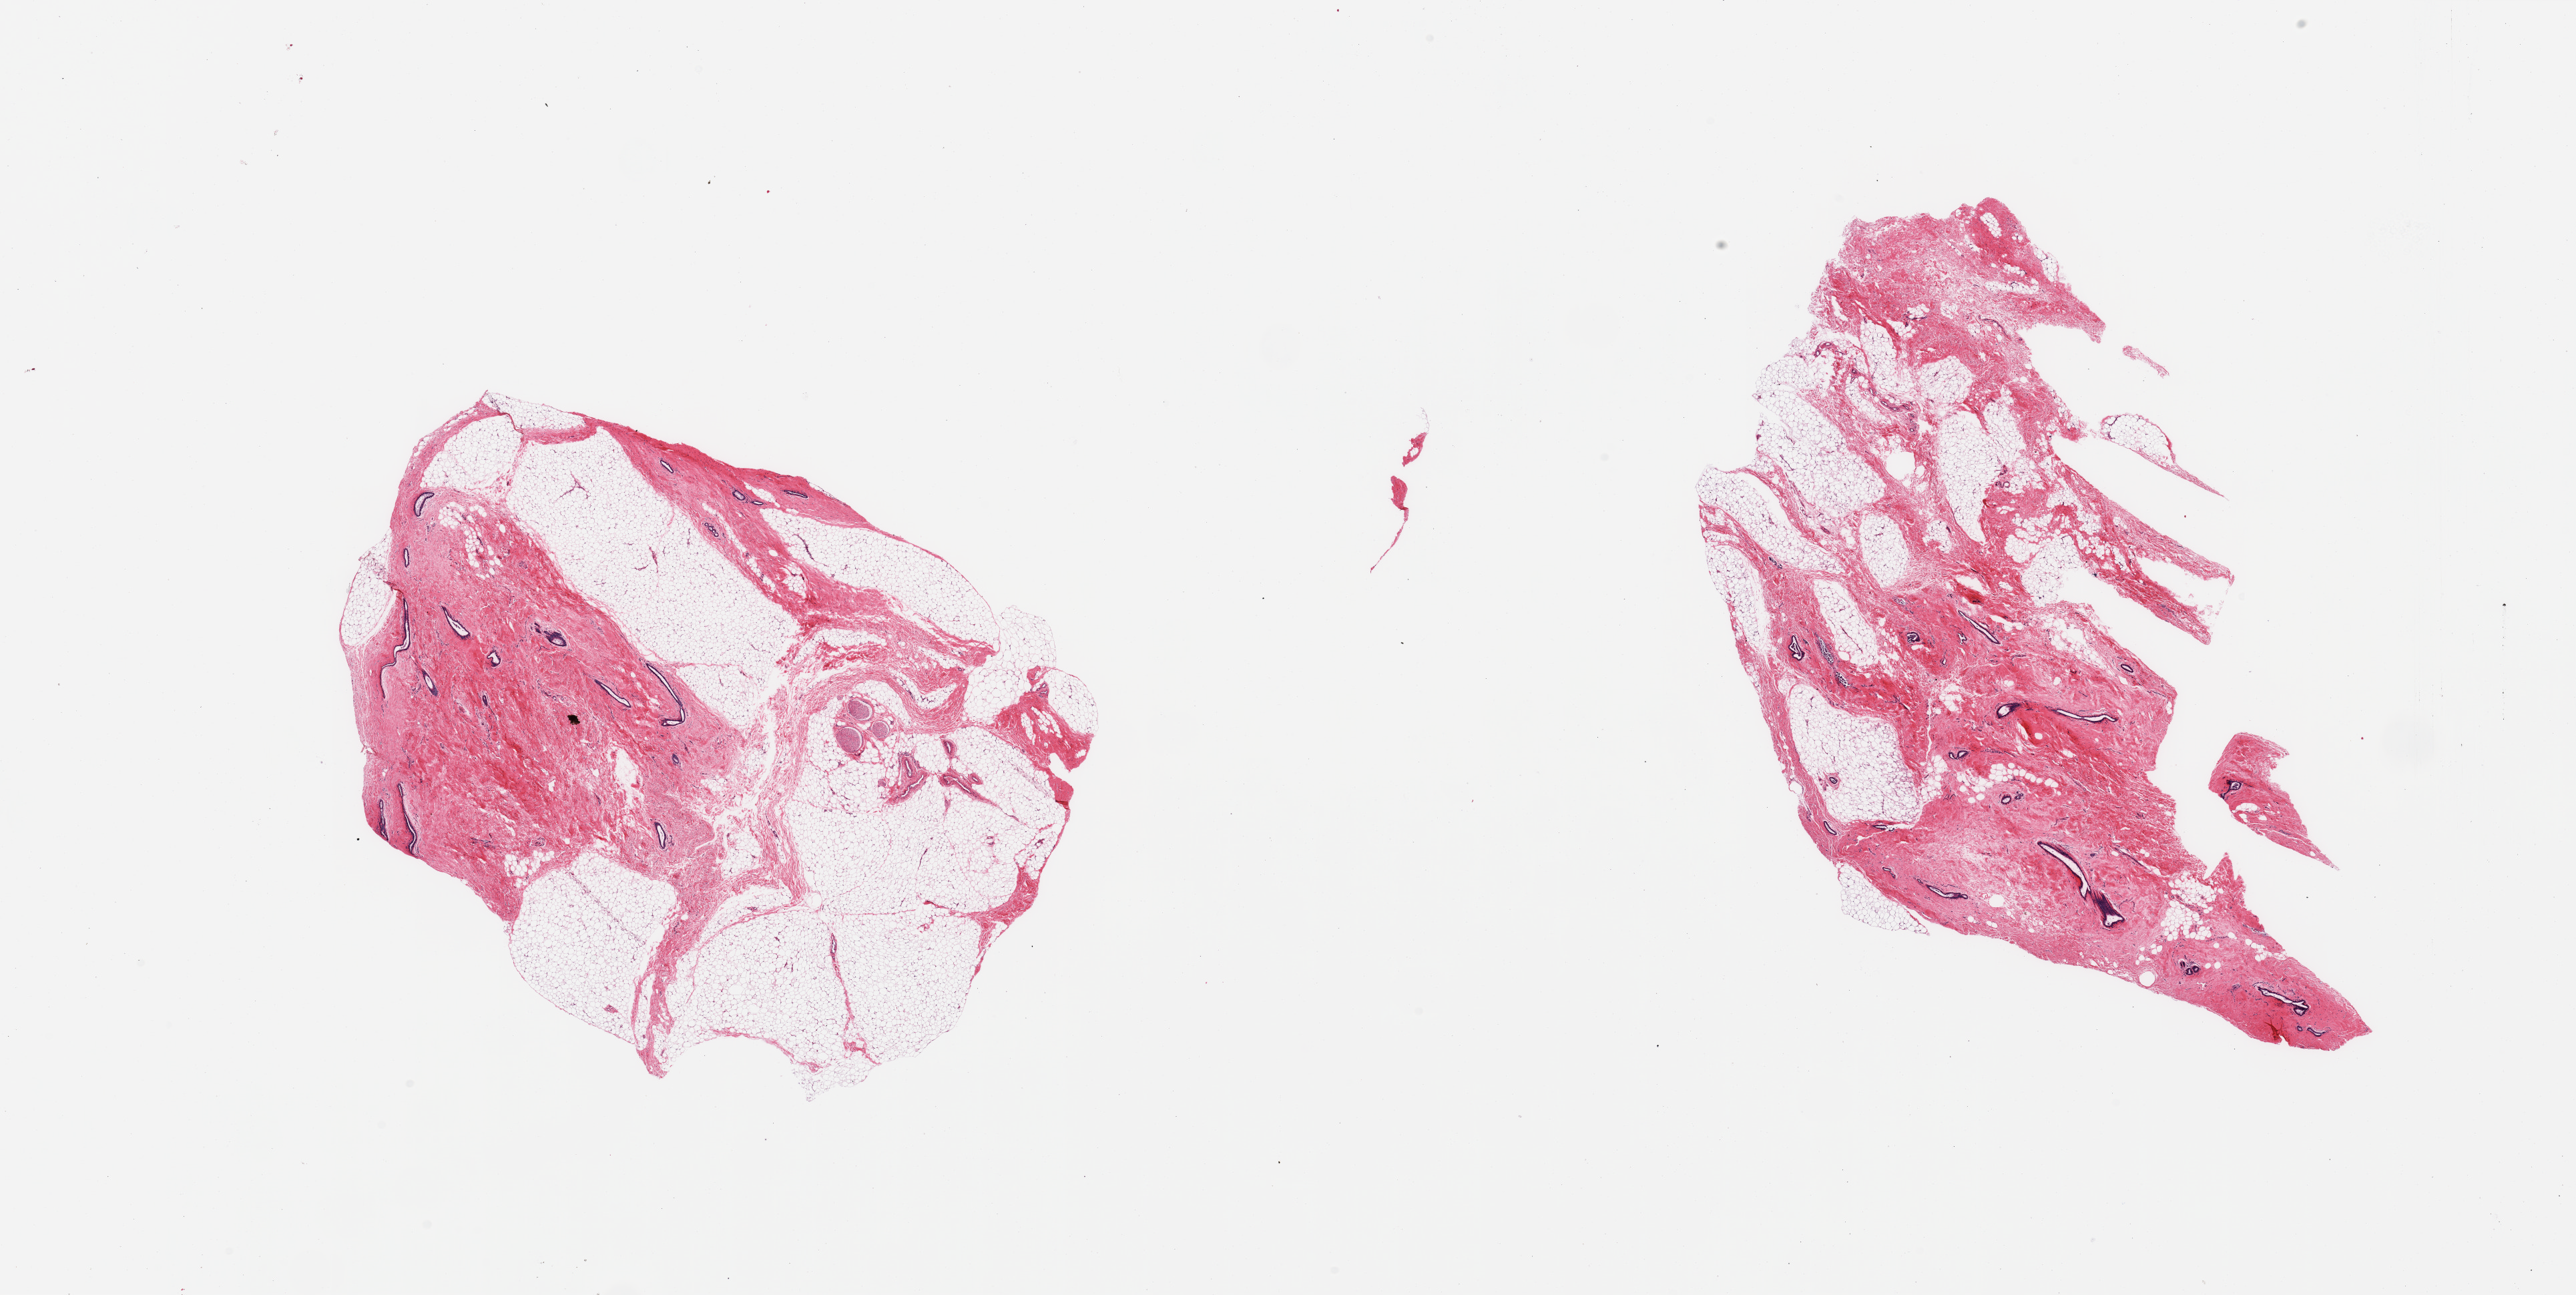
Whole-slide image, hematoxylin and eosin (H&E) stain, a low-resolution overview of the entire scanned area, about 30.5 x 15.3 mm, PAXgene-fixed paraffin-embedded (PFPE) section, target tissue: breast, donor tissue sample.
Reviewer comment on this tissue sample: 2 pieces; fibrofatty tissue with prominent slightly hyperplastic mammary ducts: gynecomastoid change.